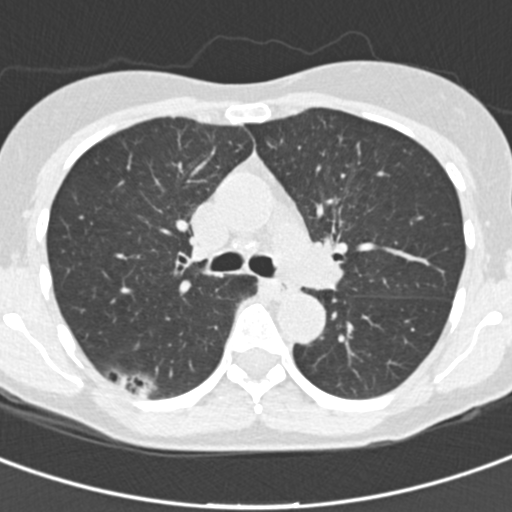
Low-dose screening chest CT, axial slice; baseline screening round; lung window (W 1500 / L -600 HU); 2 mm slice thickness; standard (soft-tissue) reconstruction kernel (B30f); slice 63 of 162 in the series; 512 × 512 image matrix. Female participant, aged 64 years at enrolment. Current smoker at enrolment.
Expert reader's lesion annotation, bounding box (x1, y1, x2, y2) in pixels: (85, 349, 177, 417). Reader record for this screening exam (exam-level; its link to the box is not recorded): non-calcified nodule or mass ≥4 mm, right lower lobe, 31 × 15 mm, poorly defined margins, ground glass attenuation. Official screen result: positive, change unspecified: nodule(s) >= 4 mm or enlarging nodule(s), mass(es), or other non-specific abnormalities suspicious for lung cancer. Participant outcome: lung cancer diagnosed 91 days after this screen — bronchiolo-alveolar carcinoma, non-mucinous, right lower lobe, well differentiated (G1), stage IA (AJCC 6th edition), 20 mm at pathology.